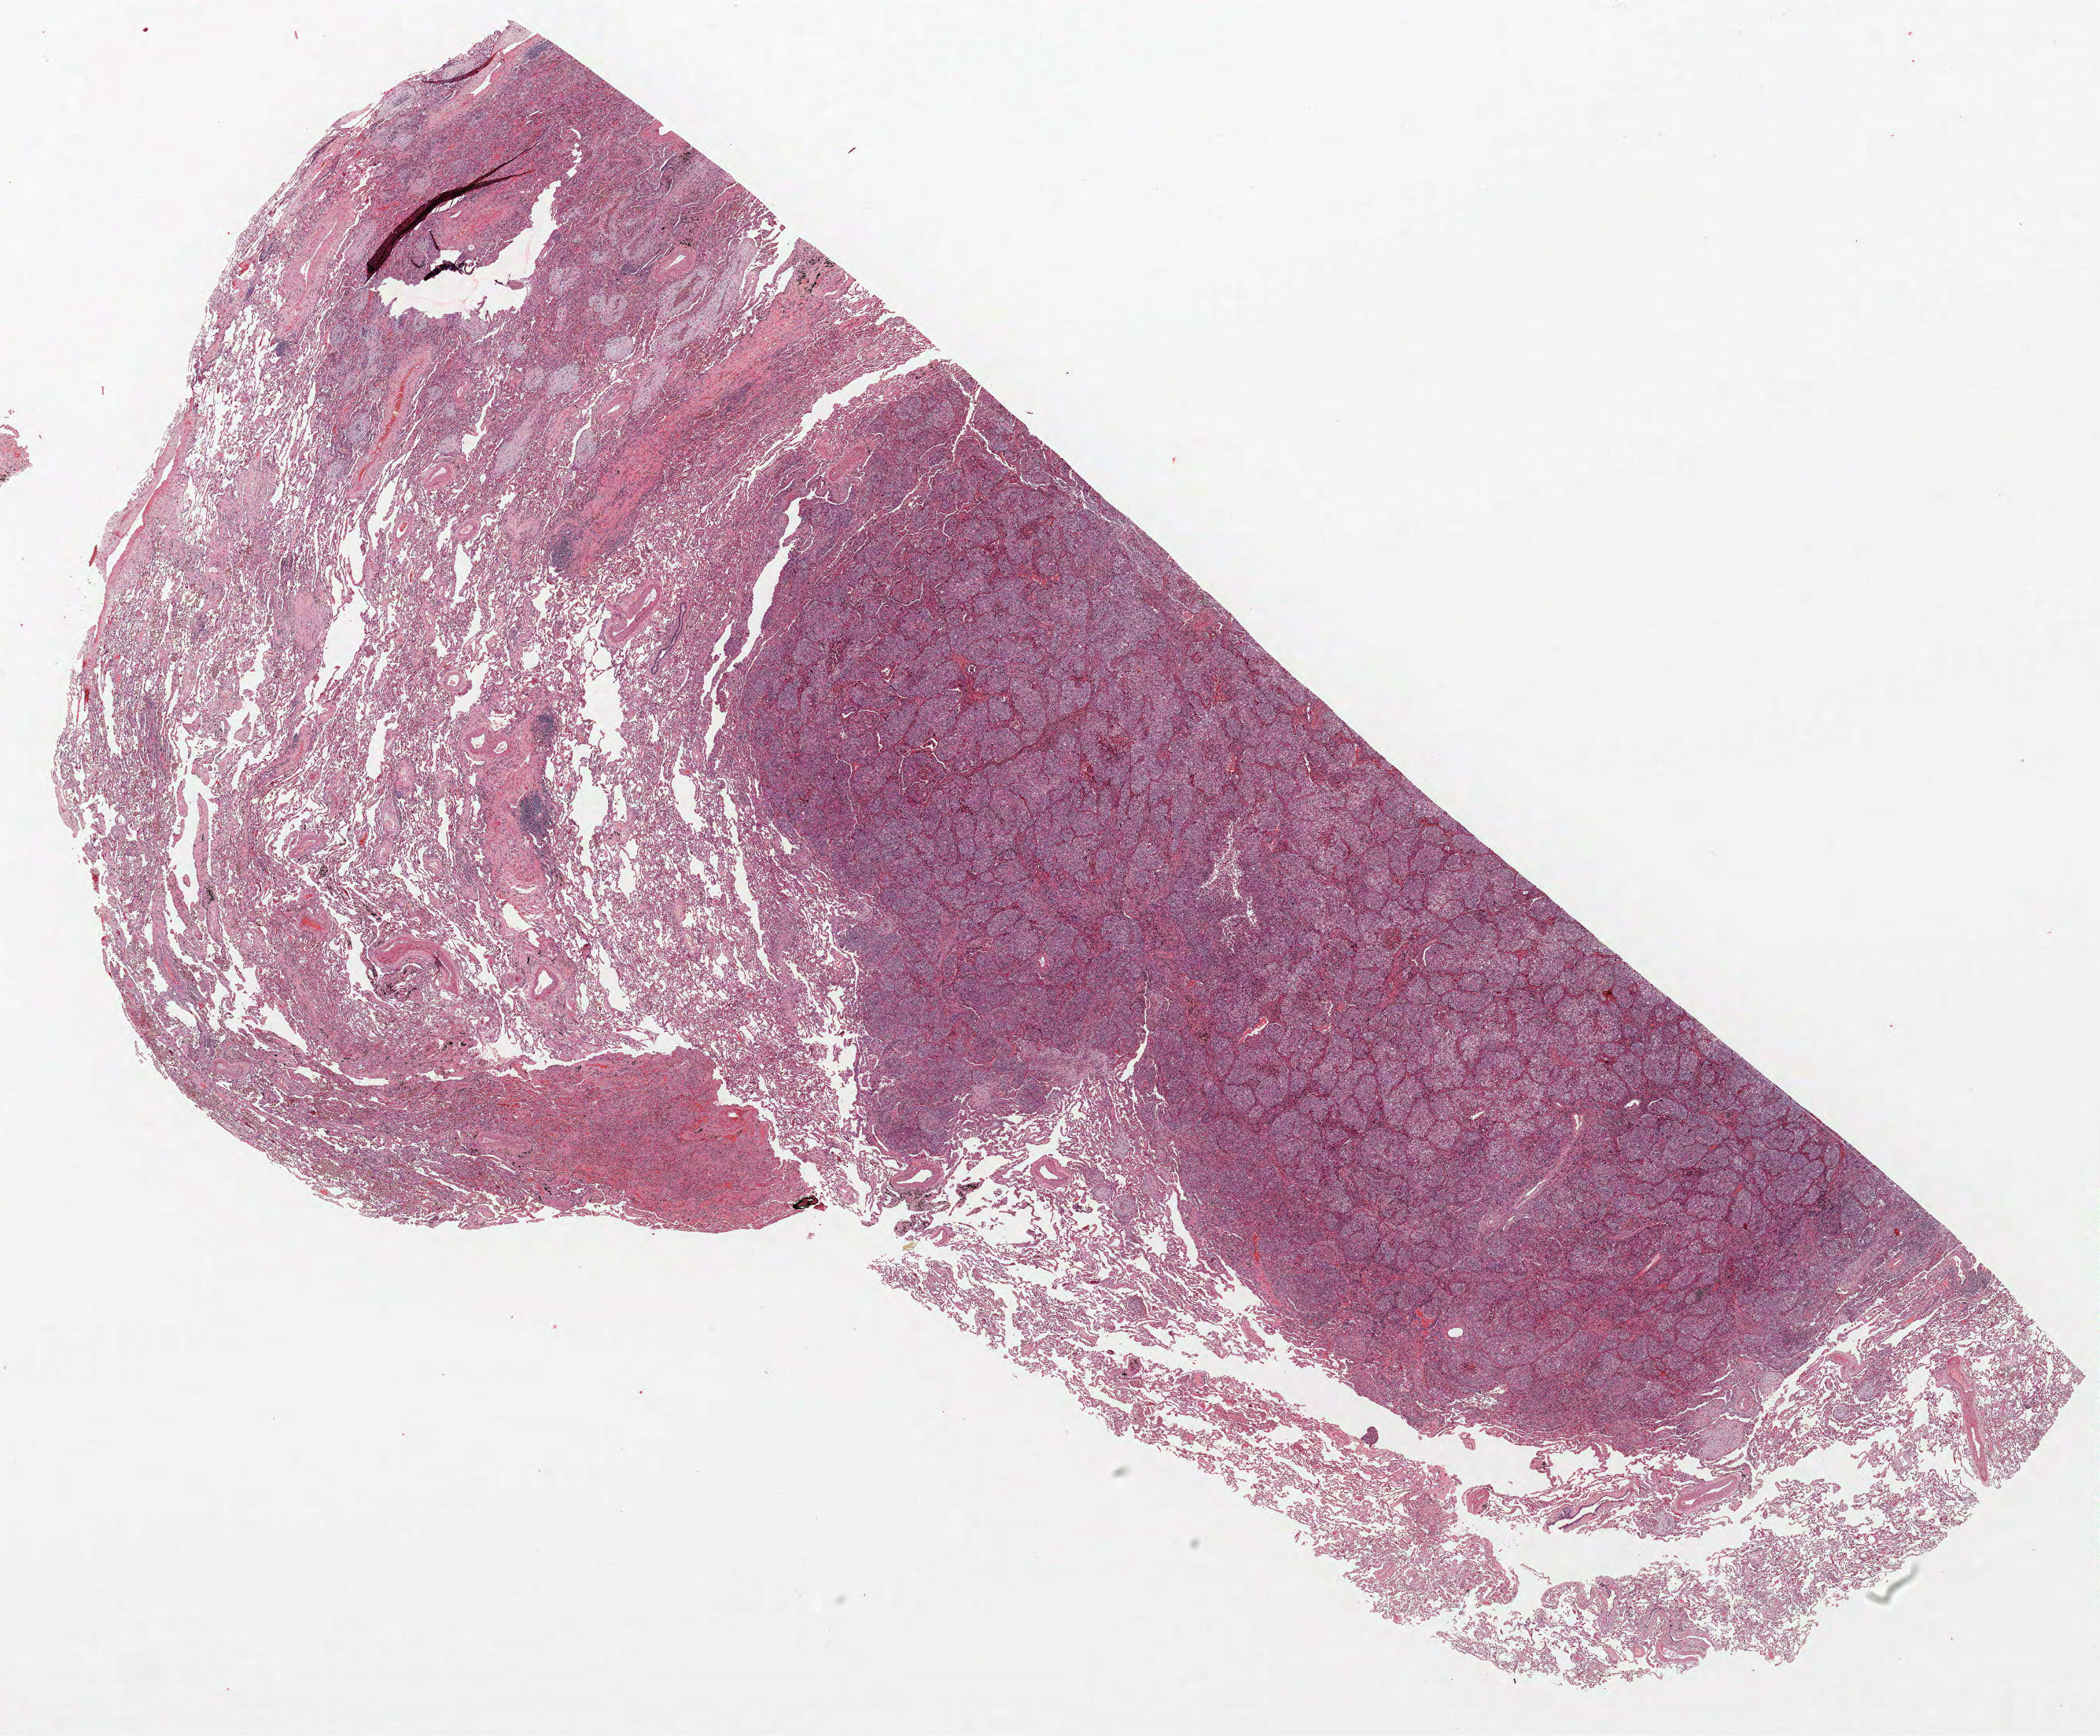
Whole-slide histology image, Hematoxylin and eosin (H&E) stained — a low-resolution overview of the entire scanned area, about 21.4 x 17.7 mm (from a 40x scan), FFPE section, lung tissue. Male, age 73 at enrolment. Grade: poorly differentiated (G3).
• participant's lung-cancer diagnosis: Adenocarcinoma, NOS
• tumour size (pathology): 30 mm
• primary tumour location (clinical record): right upper lobe
• stage (AJCC 6th edition): IIA